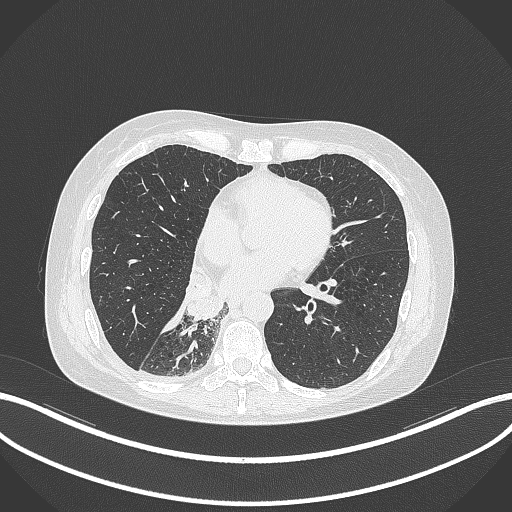
Chest CT, one axial slice. Slice 122 of 329 in the series (ordered by position). 120 kVp. Lung window (W 1500 / L -600 HU). 1 mm slice thickness. 512 × 512 image matrix, field of view 400 × 400 mm. Female patient, age 63 years. Case-level facts recorded for this patient, not image findings: clinical TNM (as recorded): T1c N0 M0.
Annotated regions visible in this slice (bounding box drawn by a radiologist):
- lung tumour (recorded histology: adenocarcinoma): bounding box [x1, y1, x2, y2] px = [180, 261, 225, 322]